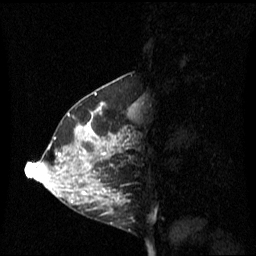
Breast MRI (dynamic contrast-enhanced), one sagittal slice. Slice 26 of 60 in the series (ordered by position). Dynamic contrast-enhanced series, image 2 of 3 at this slice position (ordered by acquisition). 1.5 T. TE 4.2 ms, TR 8.4 ms. 2.1 mm slice thickness. 256 × 256 image matrix, field of view 240 × 240 mm. Female patient, age 42 years. From the clinical record (not read from this slice): setting: breast cancer imaged before/during neoadjuvant chemotherapy; receptor status: HR-positive, HER2-negative.
Outlined on this slice (semi-automatic segmentation, software-assisted and operator-edited):
- analysis volume of interest (the breast-tissue region the enhancement analysis was run in; not a lesion): bounding box <68,102,135,201> (left, top, right, bottom; pixels)
- tumour enhancement mask (voxels above the 70 % enhancement threshold inside the analysis volume of interest): <84,114,105,195>